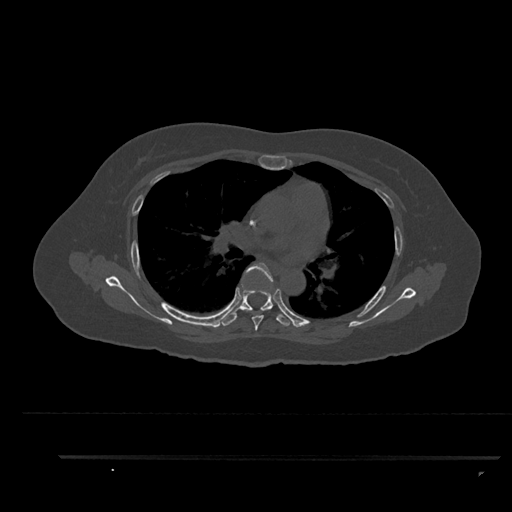
CT including the spine, one axial slice. Slice 579 of 797 in the series (ordered by position). Bone window (W 1800 / L 400 HU). 512 × 512 image matrix, field of view 408 × 408 mm. Female patient, age 44 years. Case-level facts recorded for this patient, not image findings: primary cancer: renal.
Annotated regions visible in this slice (semi-automatic segmentation, software-assisted and operator-edited):
- T5 vertebra: bounding box (x1, y1, x2, y2) in pixels: (243, 262, 274, 331)
- T6 vertebra: (222, 284, 293, 326)